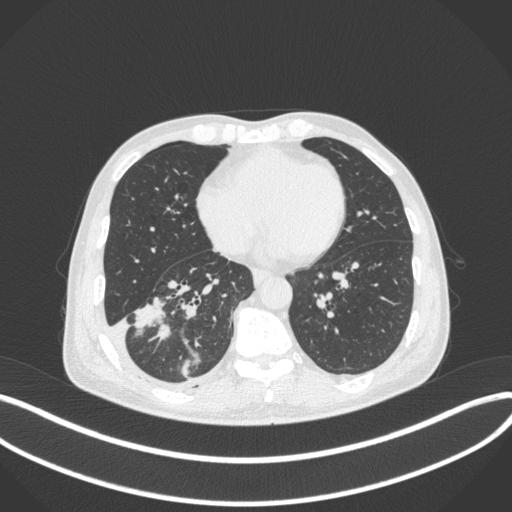
Chest CT, one axial slice; slice 143 of 385 in the series (ordered by position); 120 kVp; lung window (W 1500 / L -600 HU); 1 mm slice thickness; 512 × 512 image matrix, field of view 400 × 400 mm. Patient: male, 64 years. From the clinical record (not read from this slice): clinical TNM (as recorded): T3 N0 M0; histopathological grade: G2-3.
Structures marked on this image (rectangle marked by the reading radiologist):
- lung tumour (recorded histology: adenocarcinoma): box from (x=133, y=296) to (x=170, y=339) px